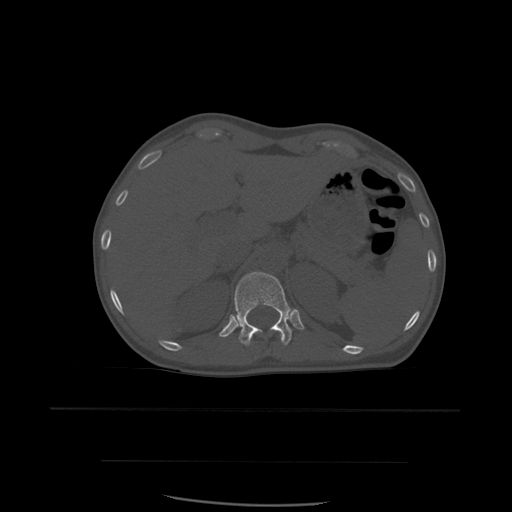
CT including the spine, one axial slice. Slice 276 of 574 in the series (ordered by position). Bone window (W 1800 / L 400 HU). 1.25 mm slice thickness. 512 × 512 image matrix, field of view 392 × 392 mm. Patient age 48 years. From the clinical record (not read from this slice): primary cancer: lung; vertebrae with lytic lesions (as recorded): T11.
Annotated regions visible in this slice (semi-automatic segmentation, software-assisted and operator-edited):
- T12 vertebra: box from (x=235, y=272) to (x=292, y=346) px